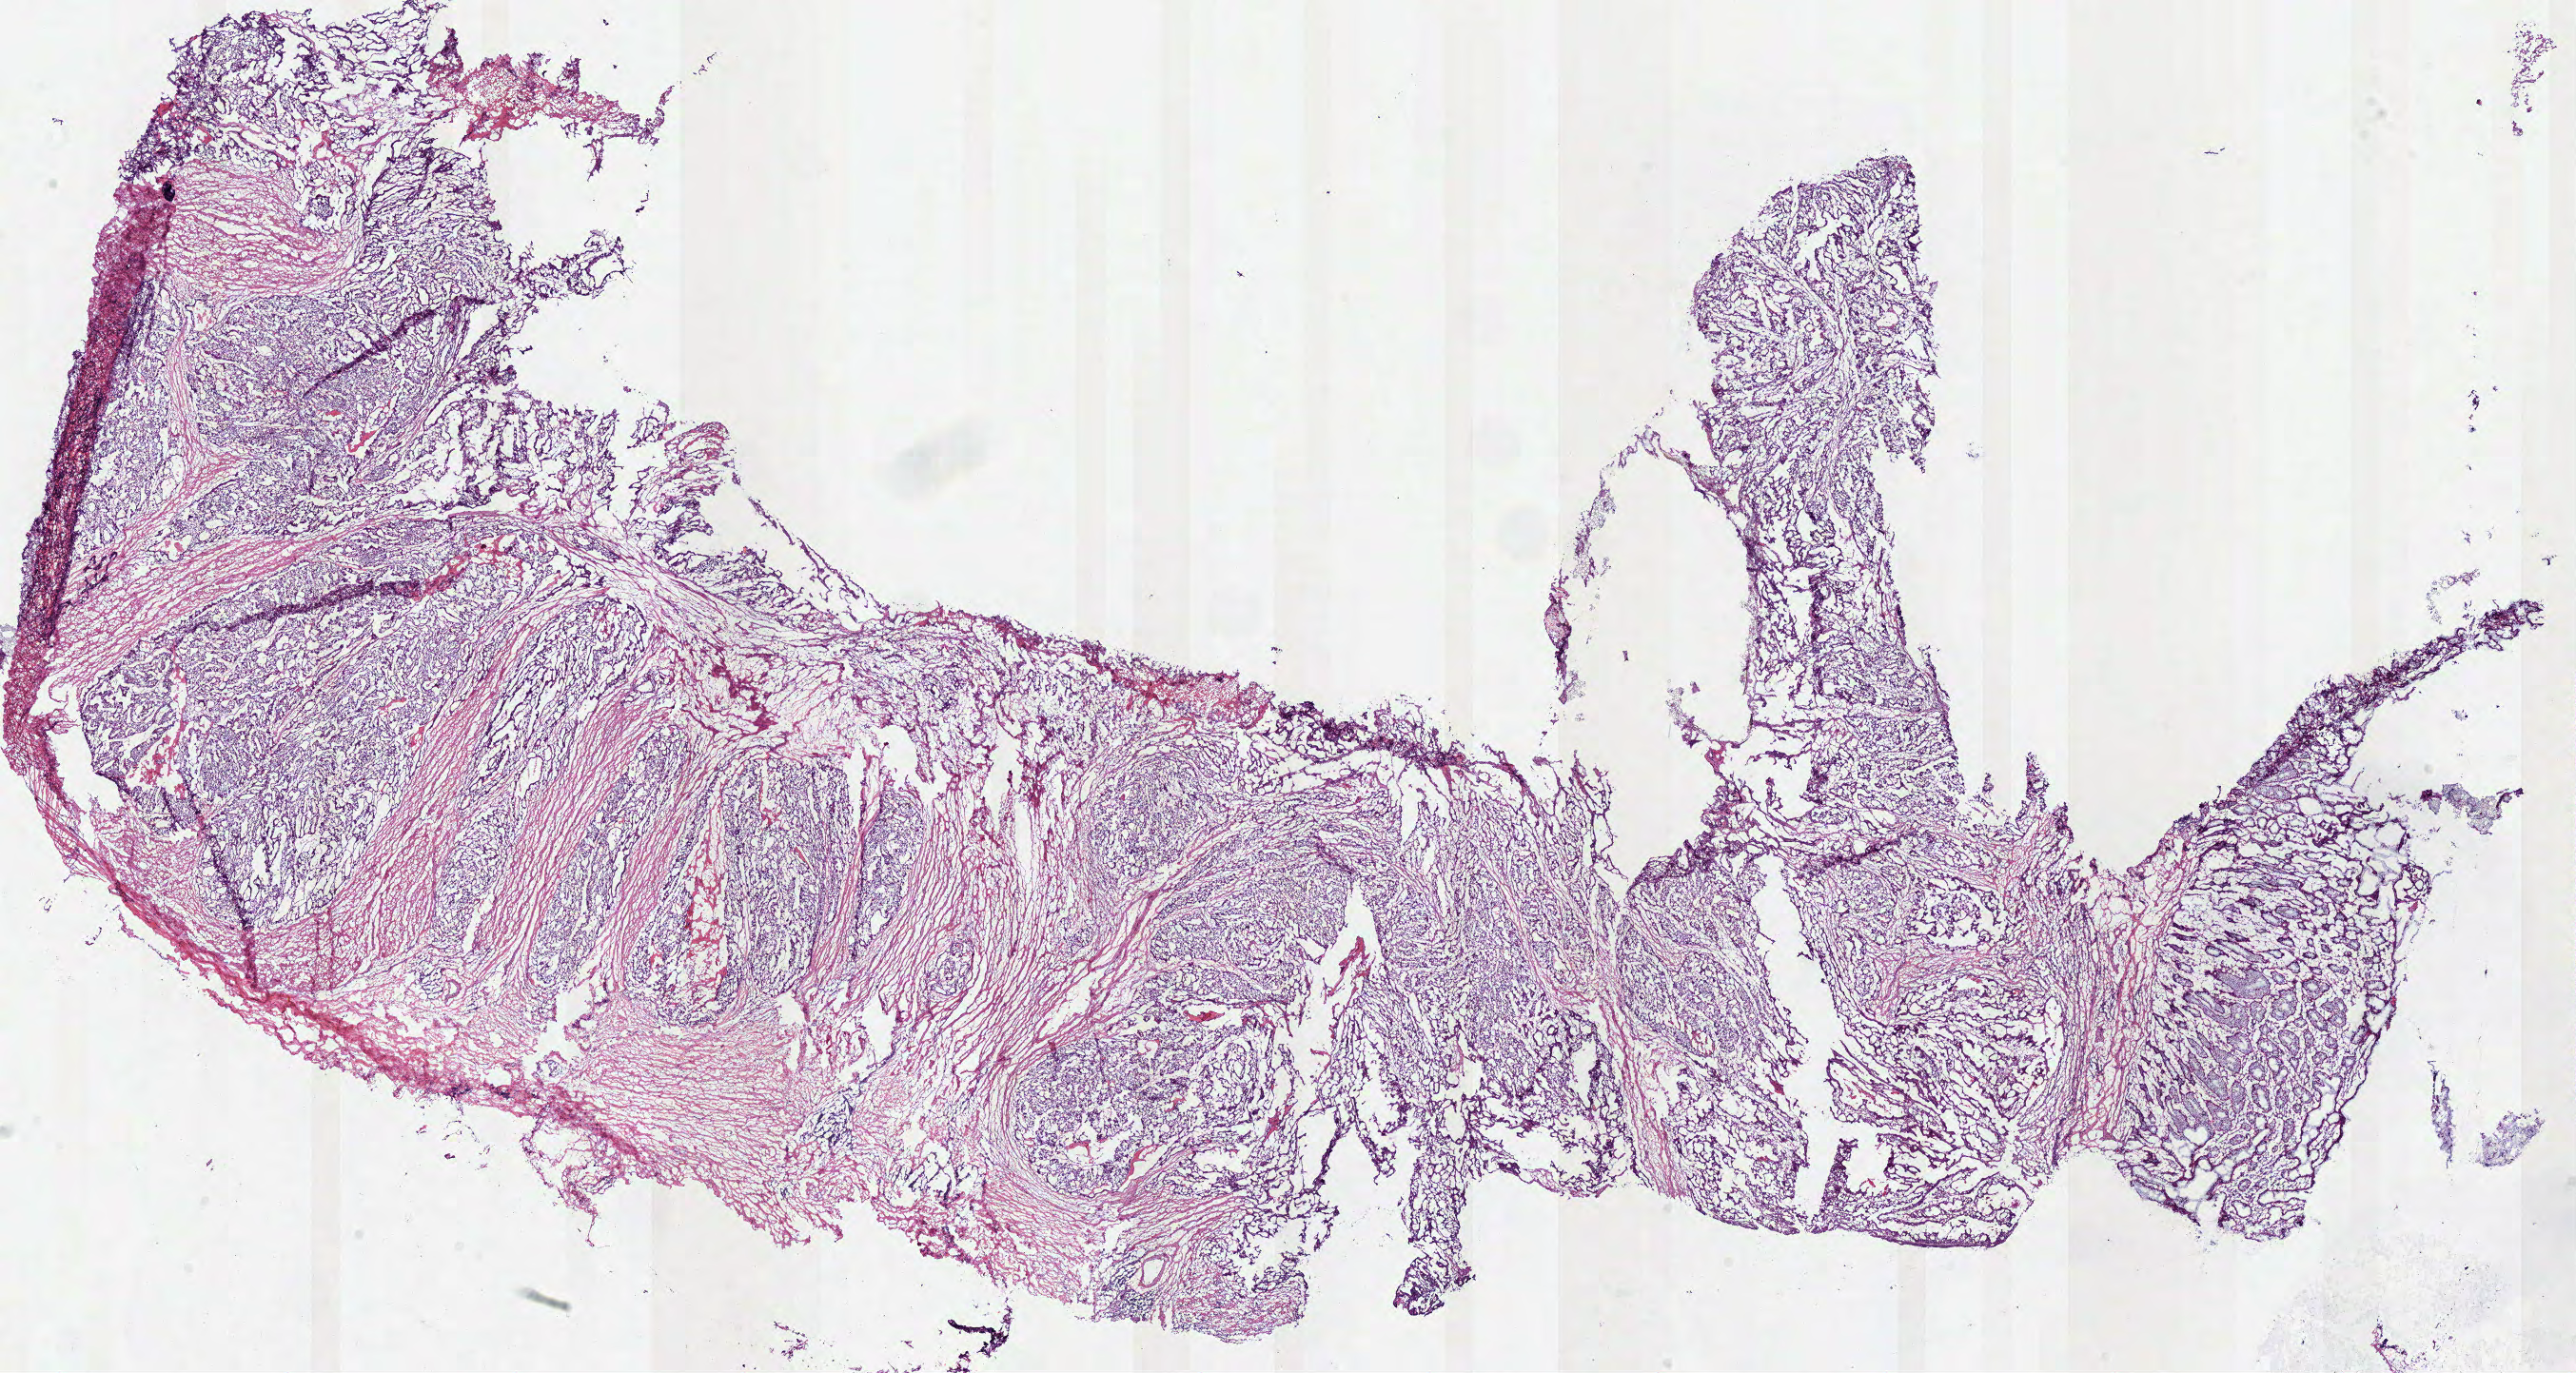
Whole-slide histology image, Hematoxylin and eosin (H&E) stained, low-resolution overview of the scanned area, about 21.3 x 11.4 mm (acquisition: 40x scan); frozen section; colon, primary tumour sample. Female patient; age at initial diagnosis 77 years. Pathologist review of this section (percent, as recorded): tumour cells 55%, tumour nuclei 80%, normal cells 5%, stromal cells 35%, necrosis 5%.
TNM: T3 N0 M0. Lymph nodes positive (case pathology): 0 of 8 examined. Pathologic diagnosis: Adenocarcinoma, NOS (sigmoid colon). AJCC pathologic stage: IIA (7th edition).